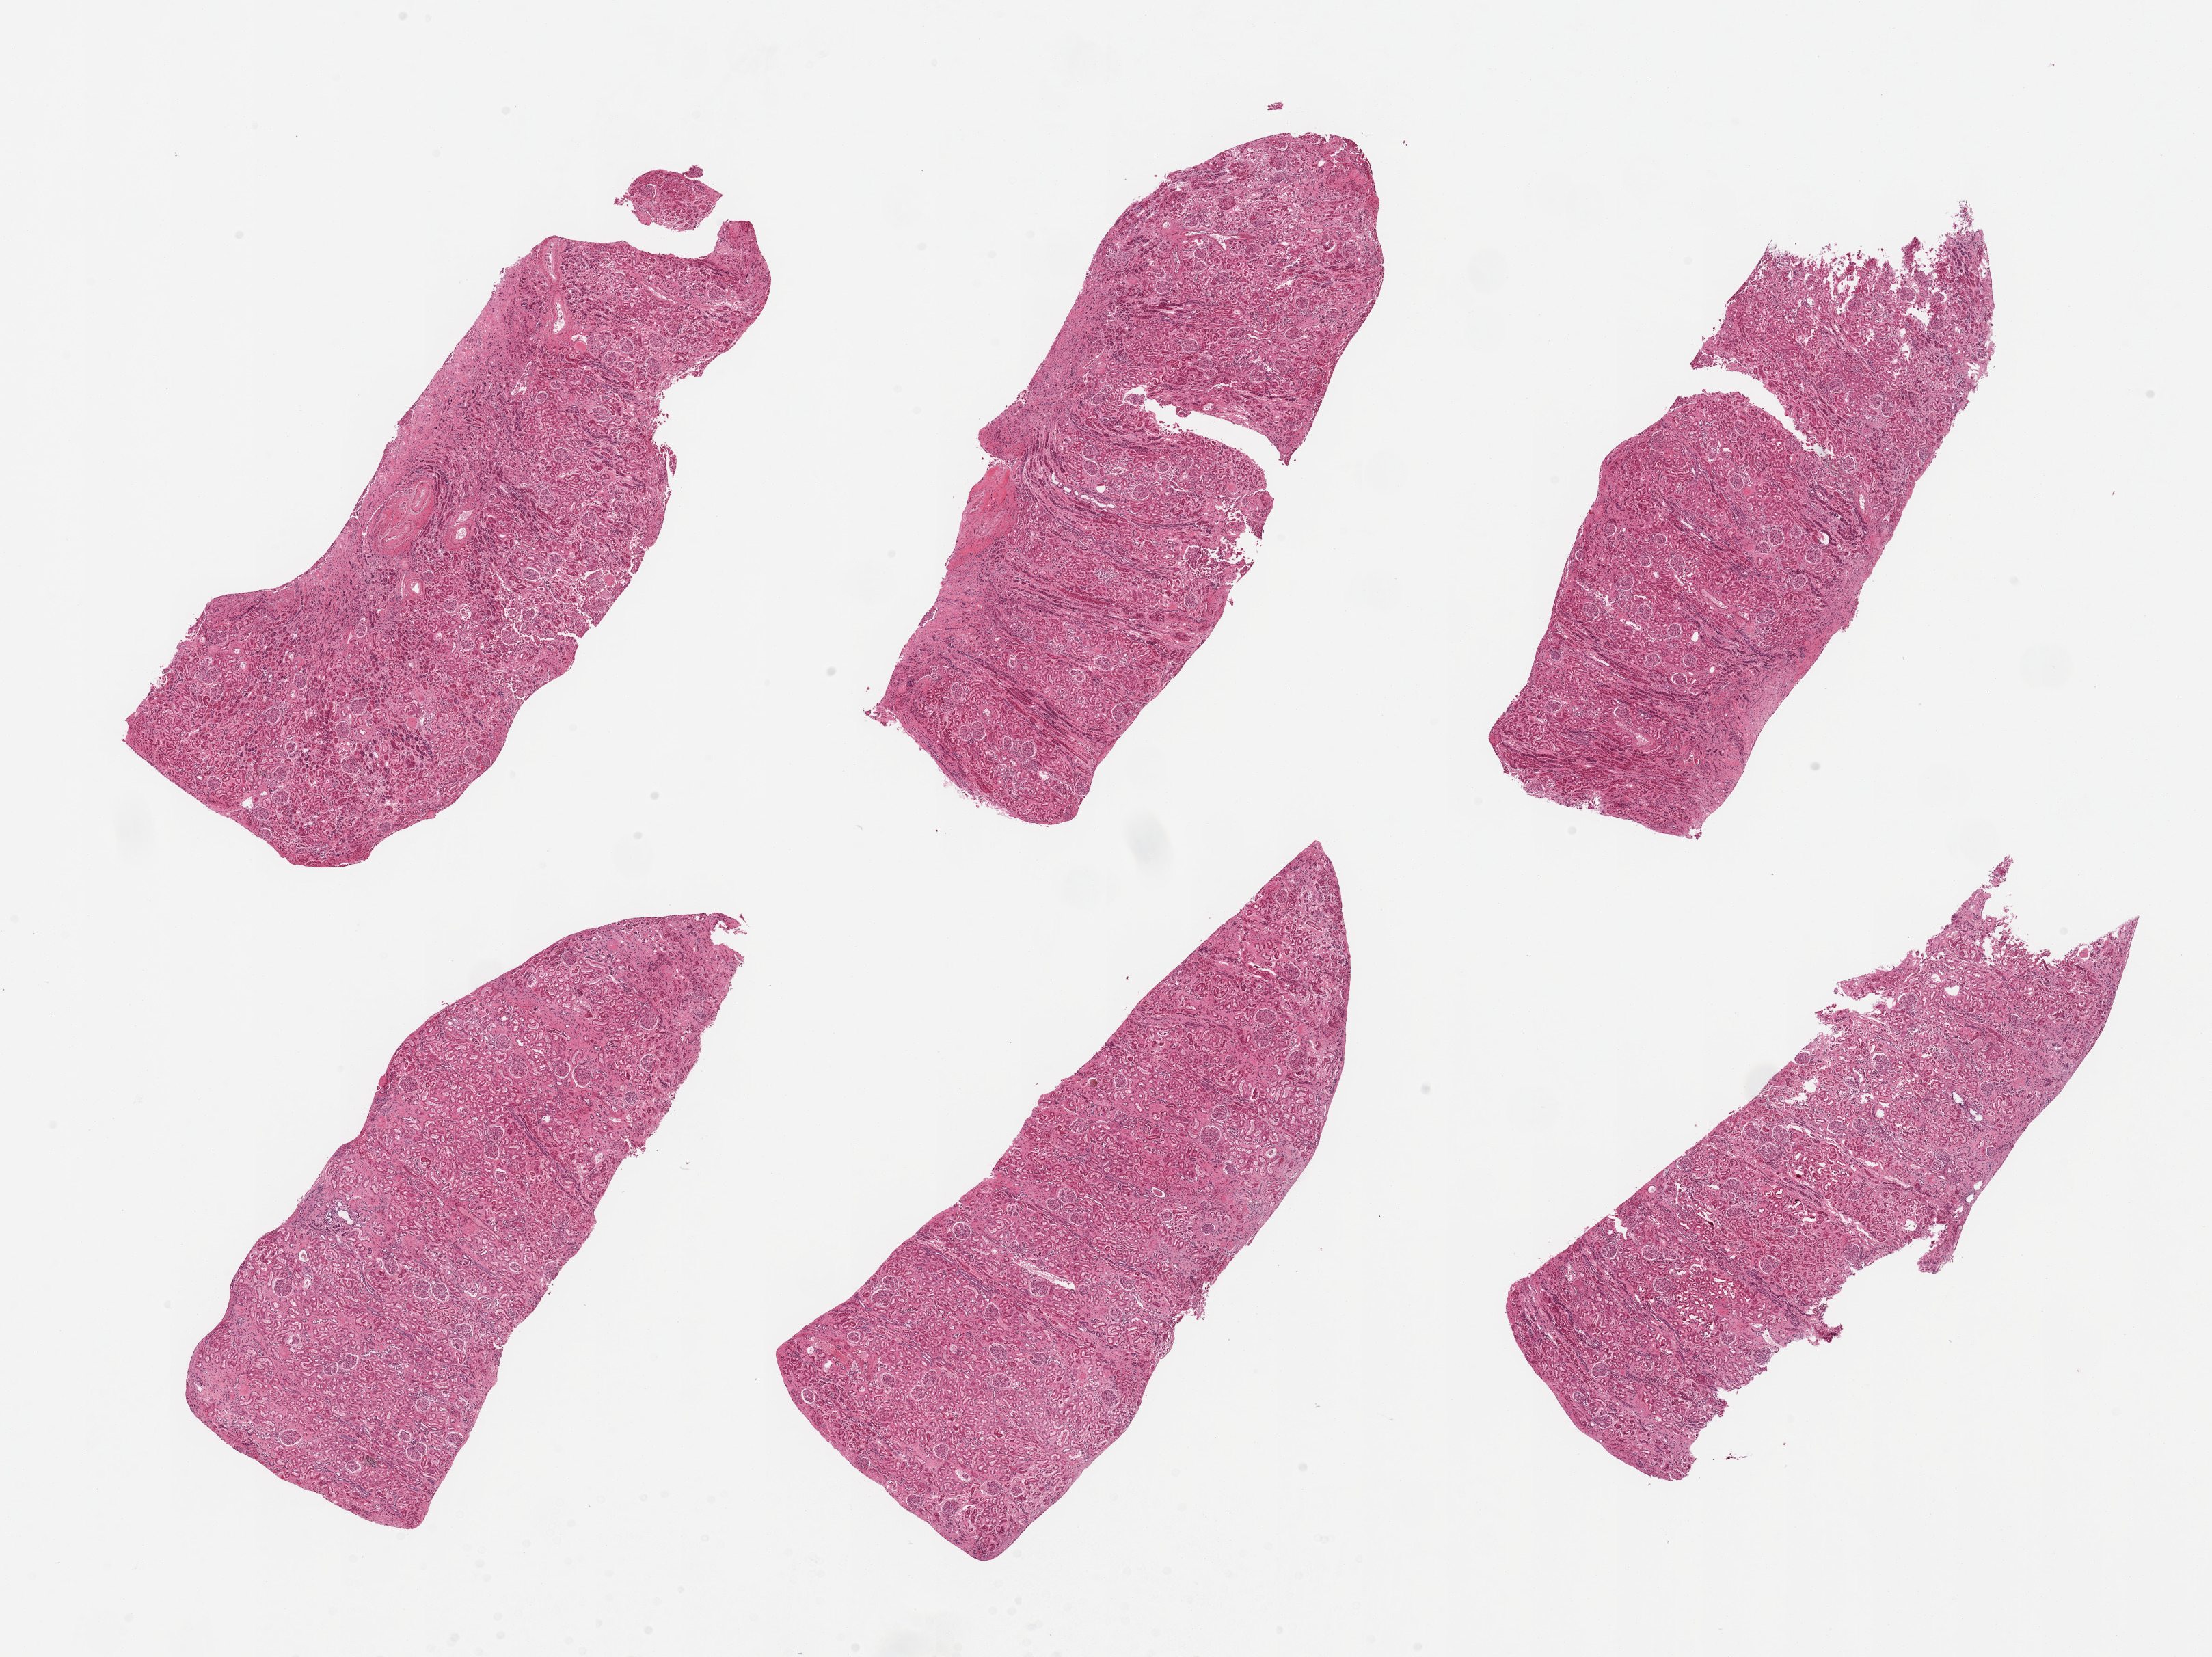
Whole-slide image, H&E stain — shown as a low-resolution overview of the whole scanned area (about 25.6 x 19.2 mm, slide scanned at 20x), PAXgene-fixed, paraffin-embedded tissue, sampled site (target tissue): renal cortex, donor tissue sample. Donor: female.
Reviewer comment on this tissue sample: 6 pieces, glomeruli present; tubules moderately autolyzed.